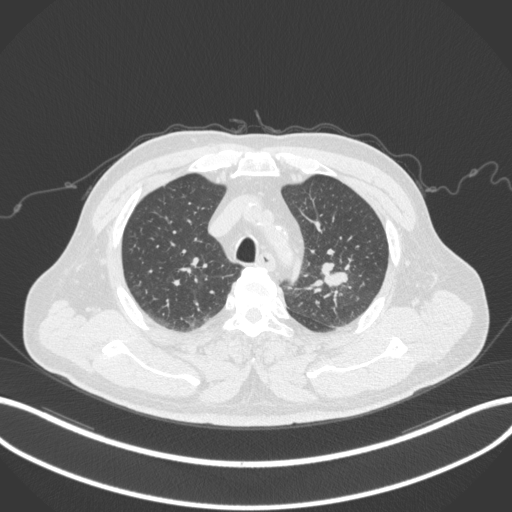
Chest CT, one axial slice. Slice 236 of 286 in the series (ordered by position). Reconstruction kernel B31f. 120 kVp. Lung window (W 1500 / L -600 HU). 1 mm slice thickness. 512 × 512 image matrix, field of view 400 × 400 mm. Male patient, age 67 years. From the clinical record (not read from this slice): clinical TNM (as recorded): T2a N1 M0; histopathological grade: G3.
Outlined on this slice (bounding box drawn by a radiologist):
- lung tumour (recorded histology: adenocarcinoma): box from (x=318, y=257) to (x=352, y=293) px